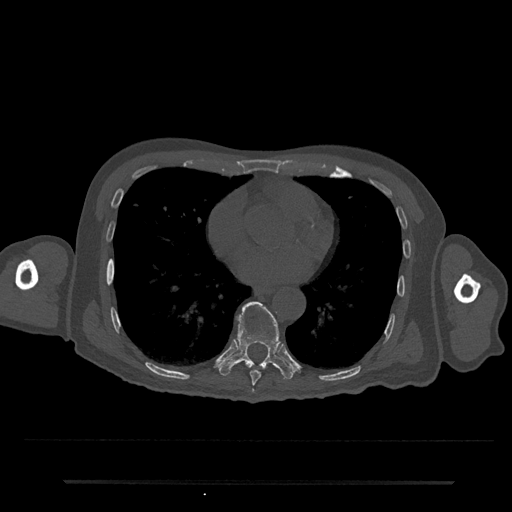
CT including the spine, one axial slice; slice 387 of 797 in the series (ordered by position); reconstruction kernel Br40s/3; 120 kVp; bone window (W 1800 / L 400 HU); 0.5 mm slice thickness; 512 × 512 image matrix. Patient: male, 74 years. From the clinical record (not read from this slice): primary cancer: prostate.
Structures marked on this image (semi-automatically segmented with operator editing):
- T8 vertebra: bounding box [x1, y1, x2, y2] px = [250, 370, 261, 386]
- T9 vertebra: [219, 301, 294, 380]